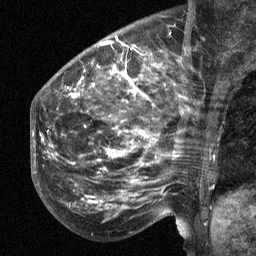
Breast MRI (dynamic contrast-enhanced), one sagittal slice. Slice 20 of 64 in the series (ordered by position). Dynamic contrast-enhanced study with each time point stored as its own series, time point 2 of 3 at this slice position (early post-contrast, ordered by acquisition time). 1.5 T. TE 4.8 ms, TR 27 ms. 2.3 mm slice thickness. 256 × 256 image matrix. Patient: female, 50 years. Case-level facts recorded for this patient, not image findings: setting: breast cancer imaged before/during neoadjuvant chemotherapy; receptor status: HER2-positive.
Outlined on this slice (semi-automatic segmentation, software-assisted and operator-edited):
- analysis volume of interest (the breast-tissue region the enhancement analysis was run in; not a lesion): box from (x=53, y=64) to (x=211, y=218) px
- tumour enhancement mask (voxels above the 90 % enhancement threshold inside the analysis volume of interest): (x=56, y=65)–(x=180, y=204)